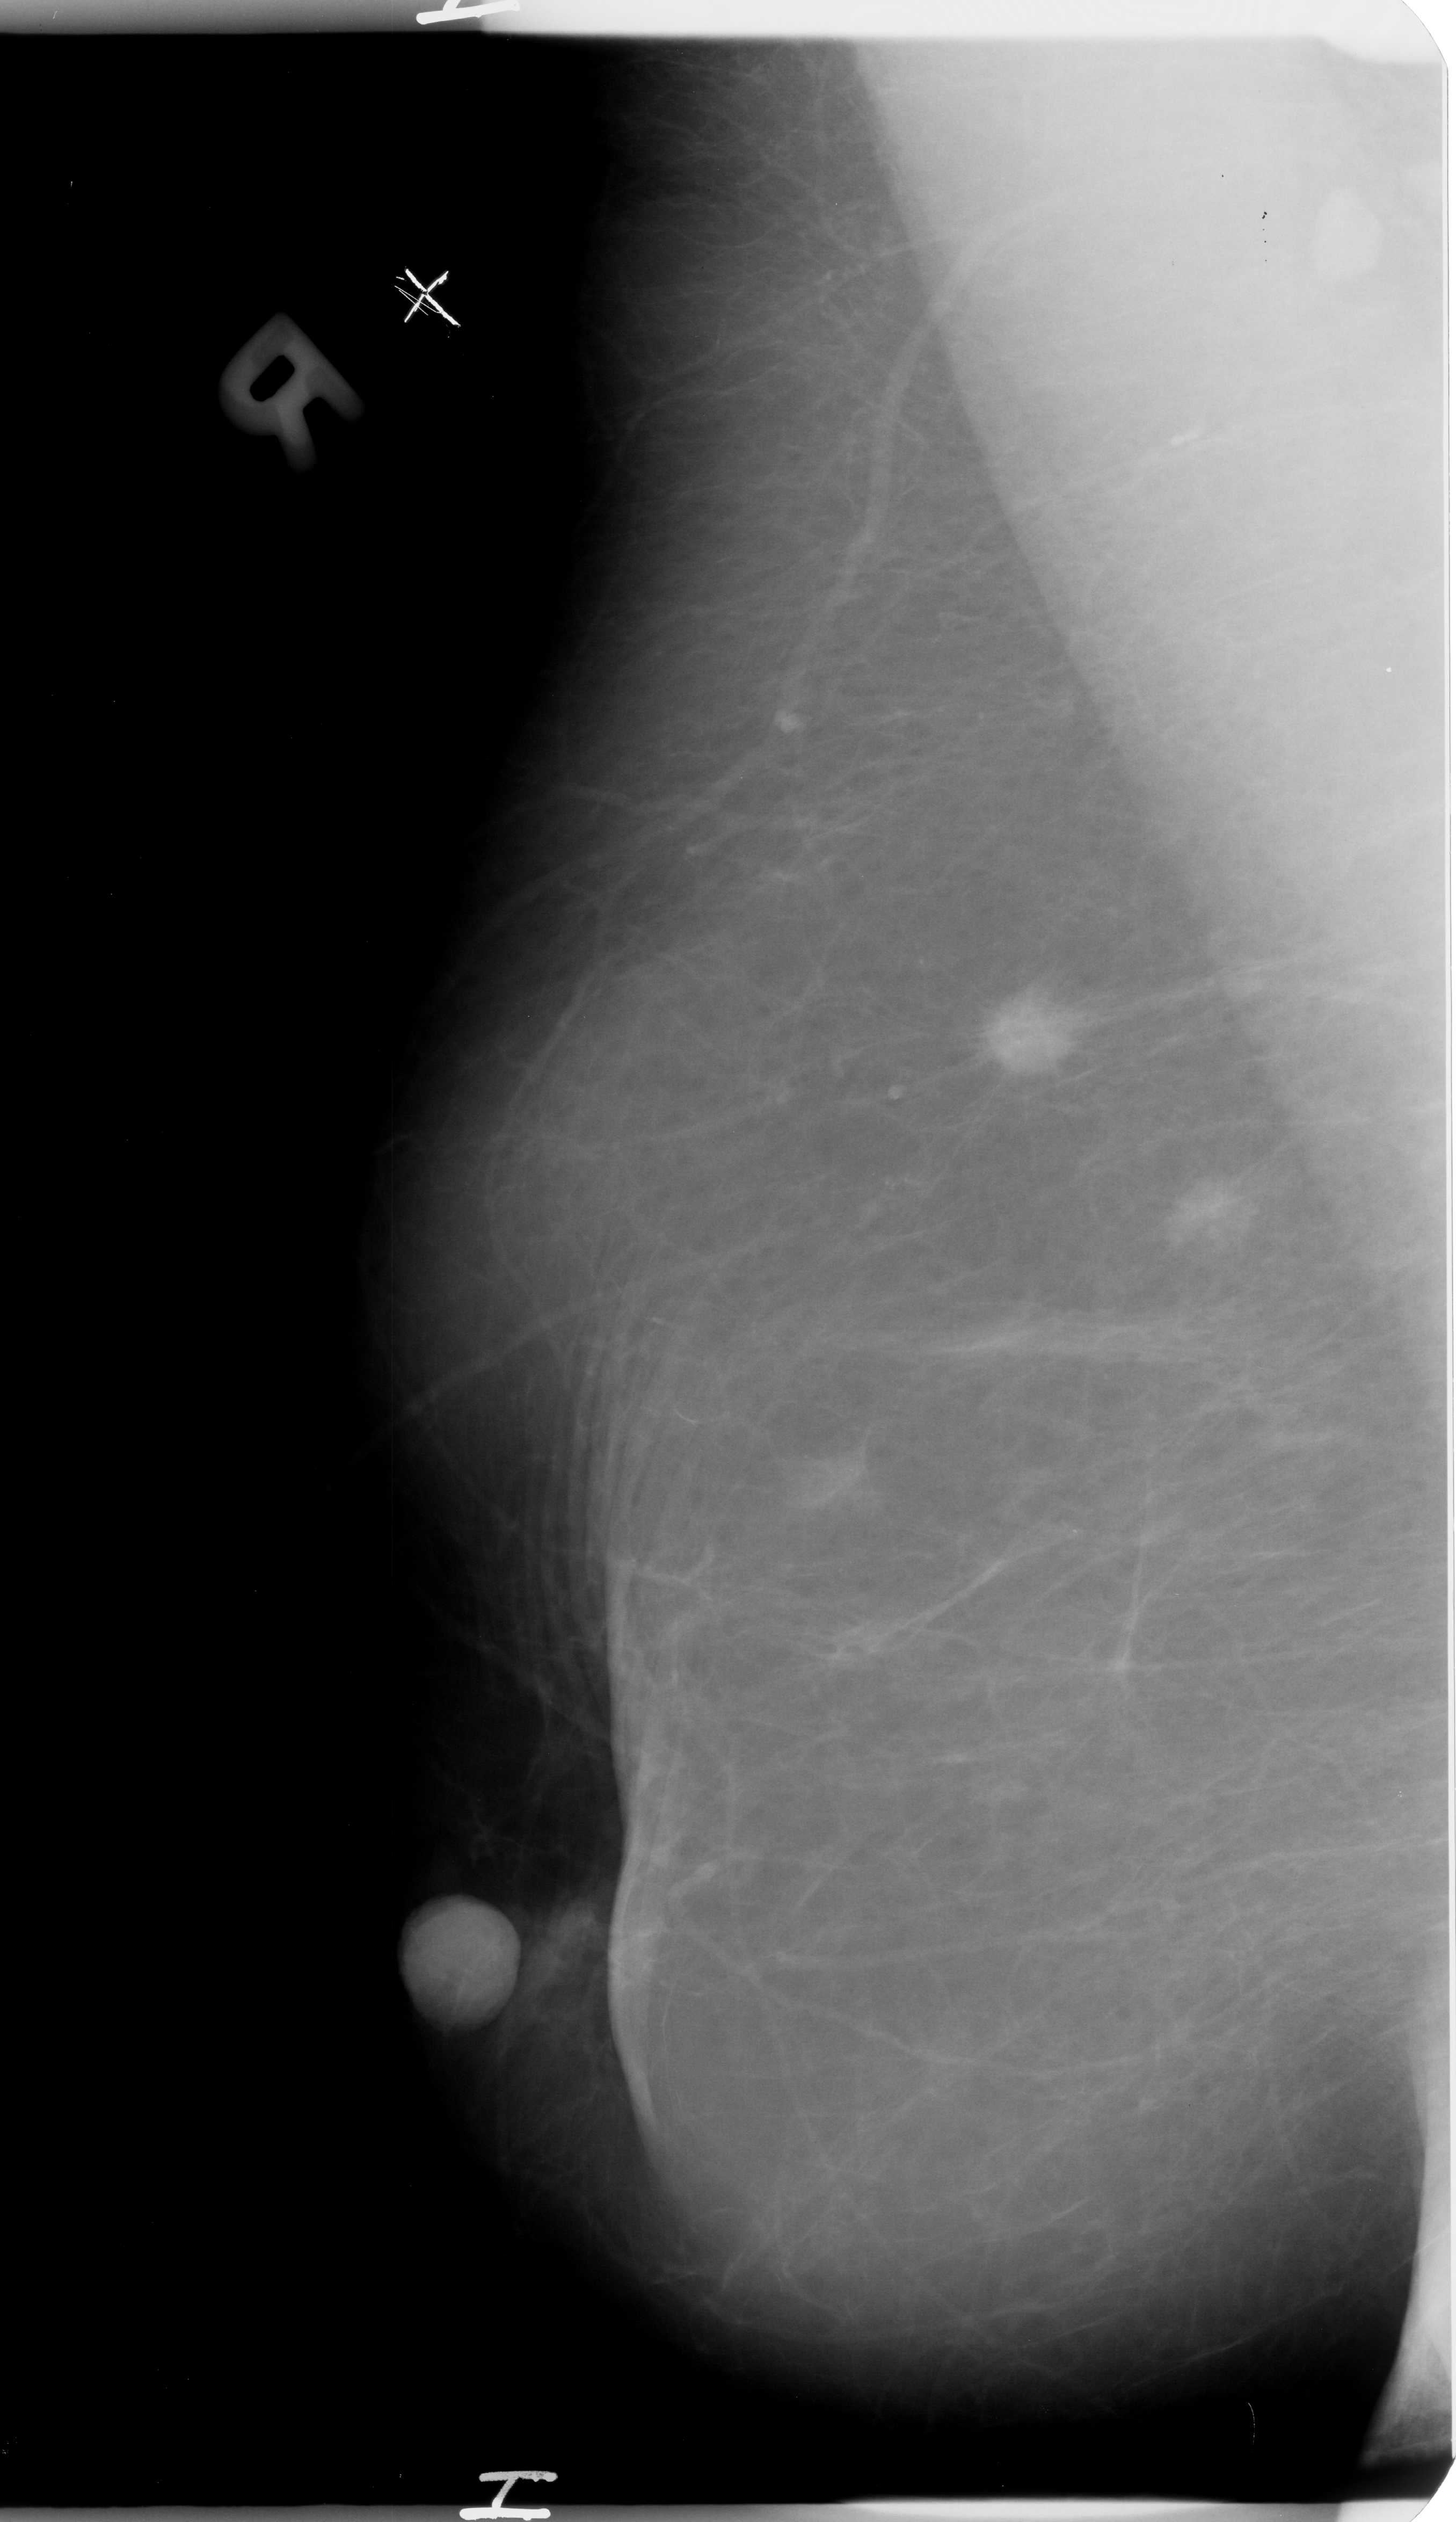
Mammogram (digitized film). Right breast. MLO view. 1456 × 2522 image matrix.
Expert-marked regions of interest on this image (one box per marked abnormality):
- mass, shape irregular, margins spiculated; BI-RADS assessment category 4; subtlety rating 5 on a 1 (subtle) to 5 (obvious) scale; pathology (as recorded): malignant: bounding box <976,990,1074,1071> (left, top, right, bottom; pixels)